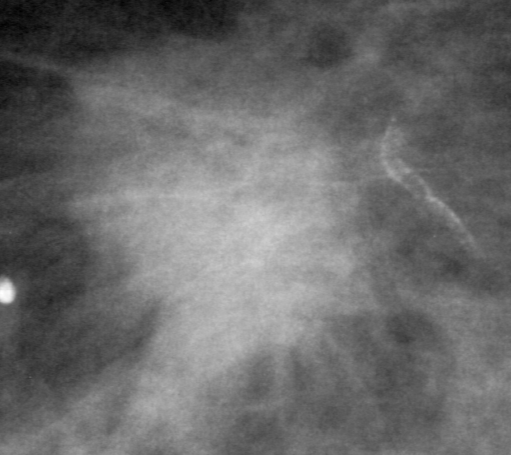
Crop from a digitized film mammogram around one marked abnormality, left breast, MLO view, BI-RADS breast density category 3 (scale 1–4).
- Marked abnormality: mass, shape irregular, margins spiculated; BI-RADS assessment category 5; subtlety rating 5 on a 1 (subtle) to 5 (obvious) scale; pathology result (as recorded, not read from the image): malignant.